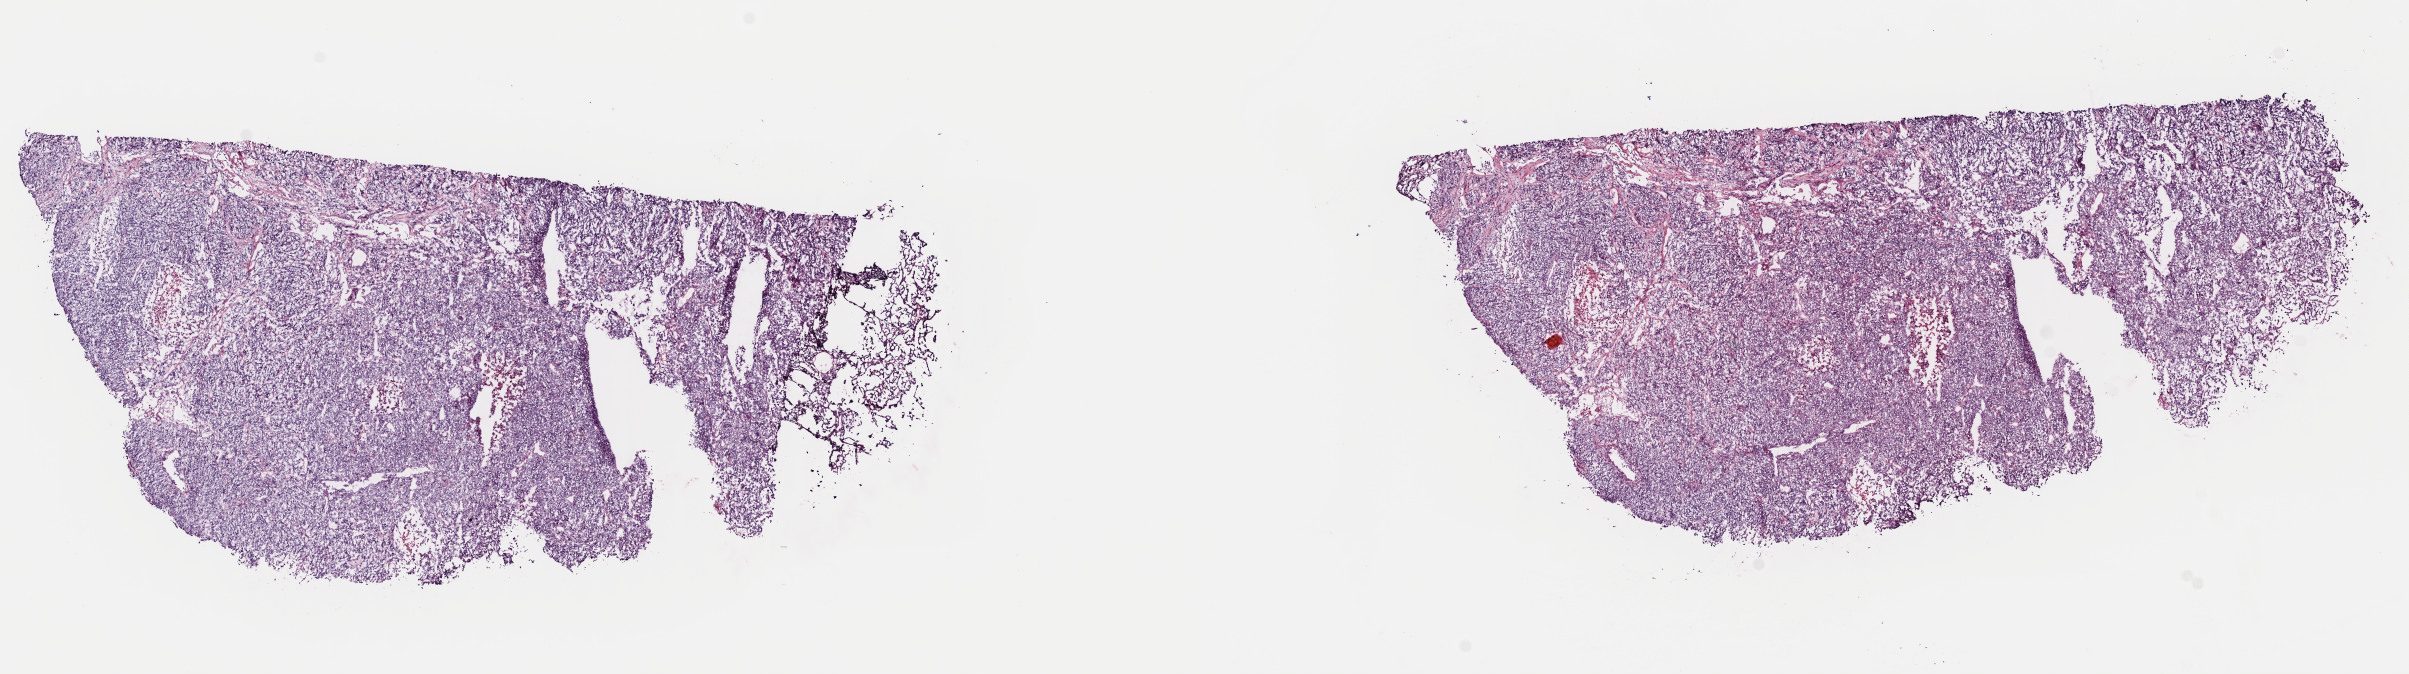
H&E-stained whole-slide image — a low-resolution overview of the entire scanned area, about 19.0 x 5.3 mm, frozen section from the top of the tissue portion, metastatic tumour sample, sampled site not recorded. Male, age 49 years at initial diagnosis. Composition of this section per pathologist review: tumour cells 95%, tumour nuclei 80%, normal cells 0%, stromal cells 0%, necrosis 5%. Inflammatory infiltration, as recorded: lymphocyte infiltration 1%, monocyte infiltration 0%, neutrophil infiltration 0%.
This section: metastatic tumour tissue. Patient diagnosis: Malignant melanoma, NOS.